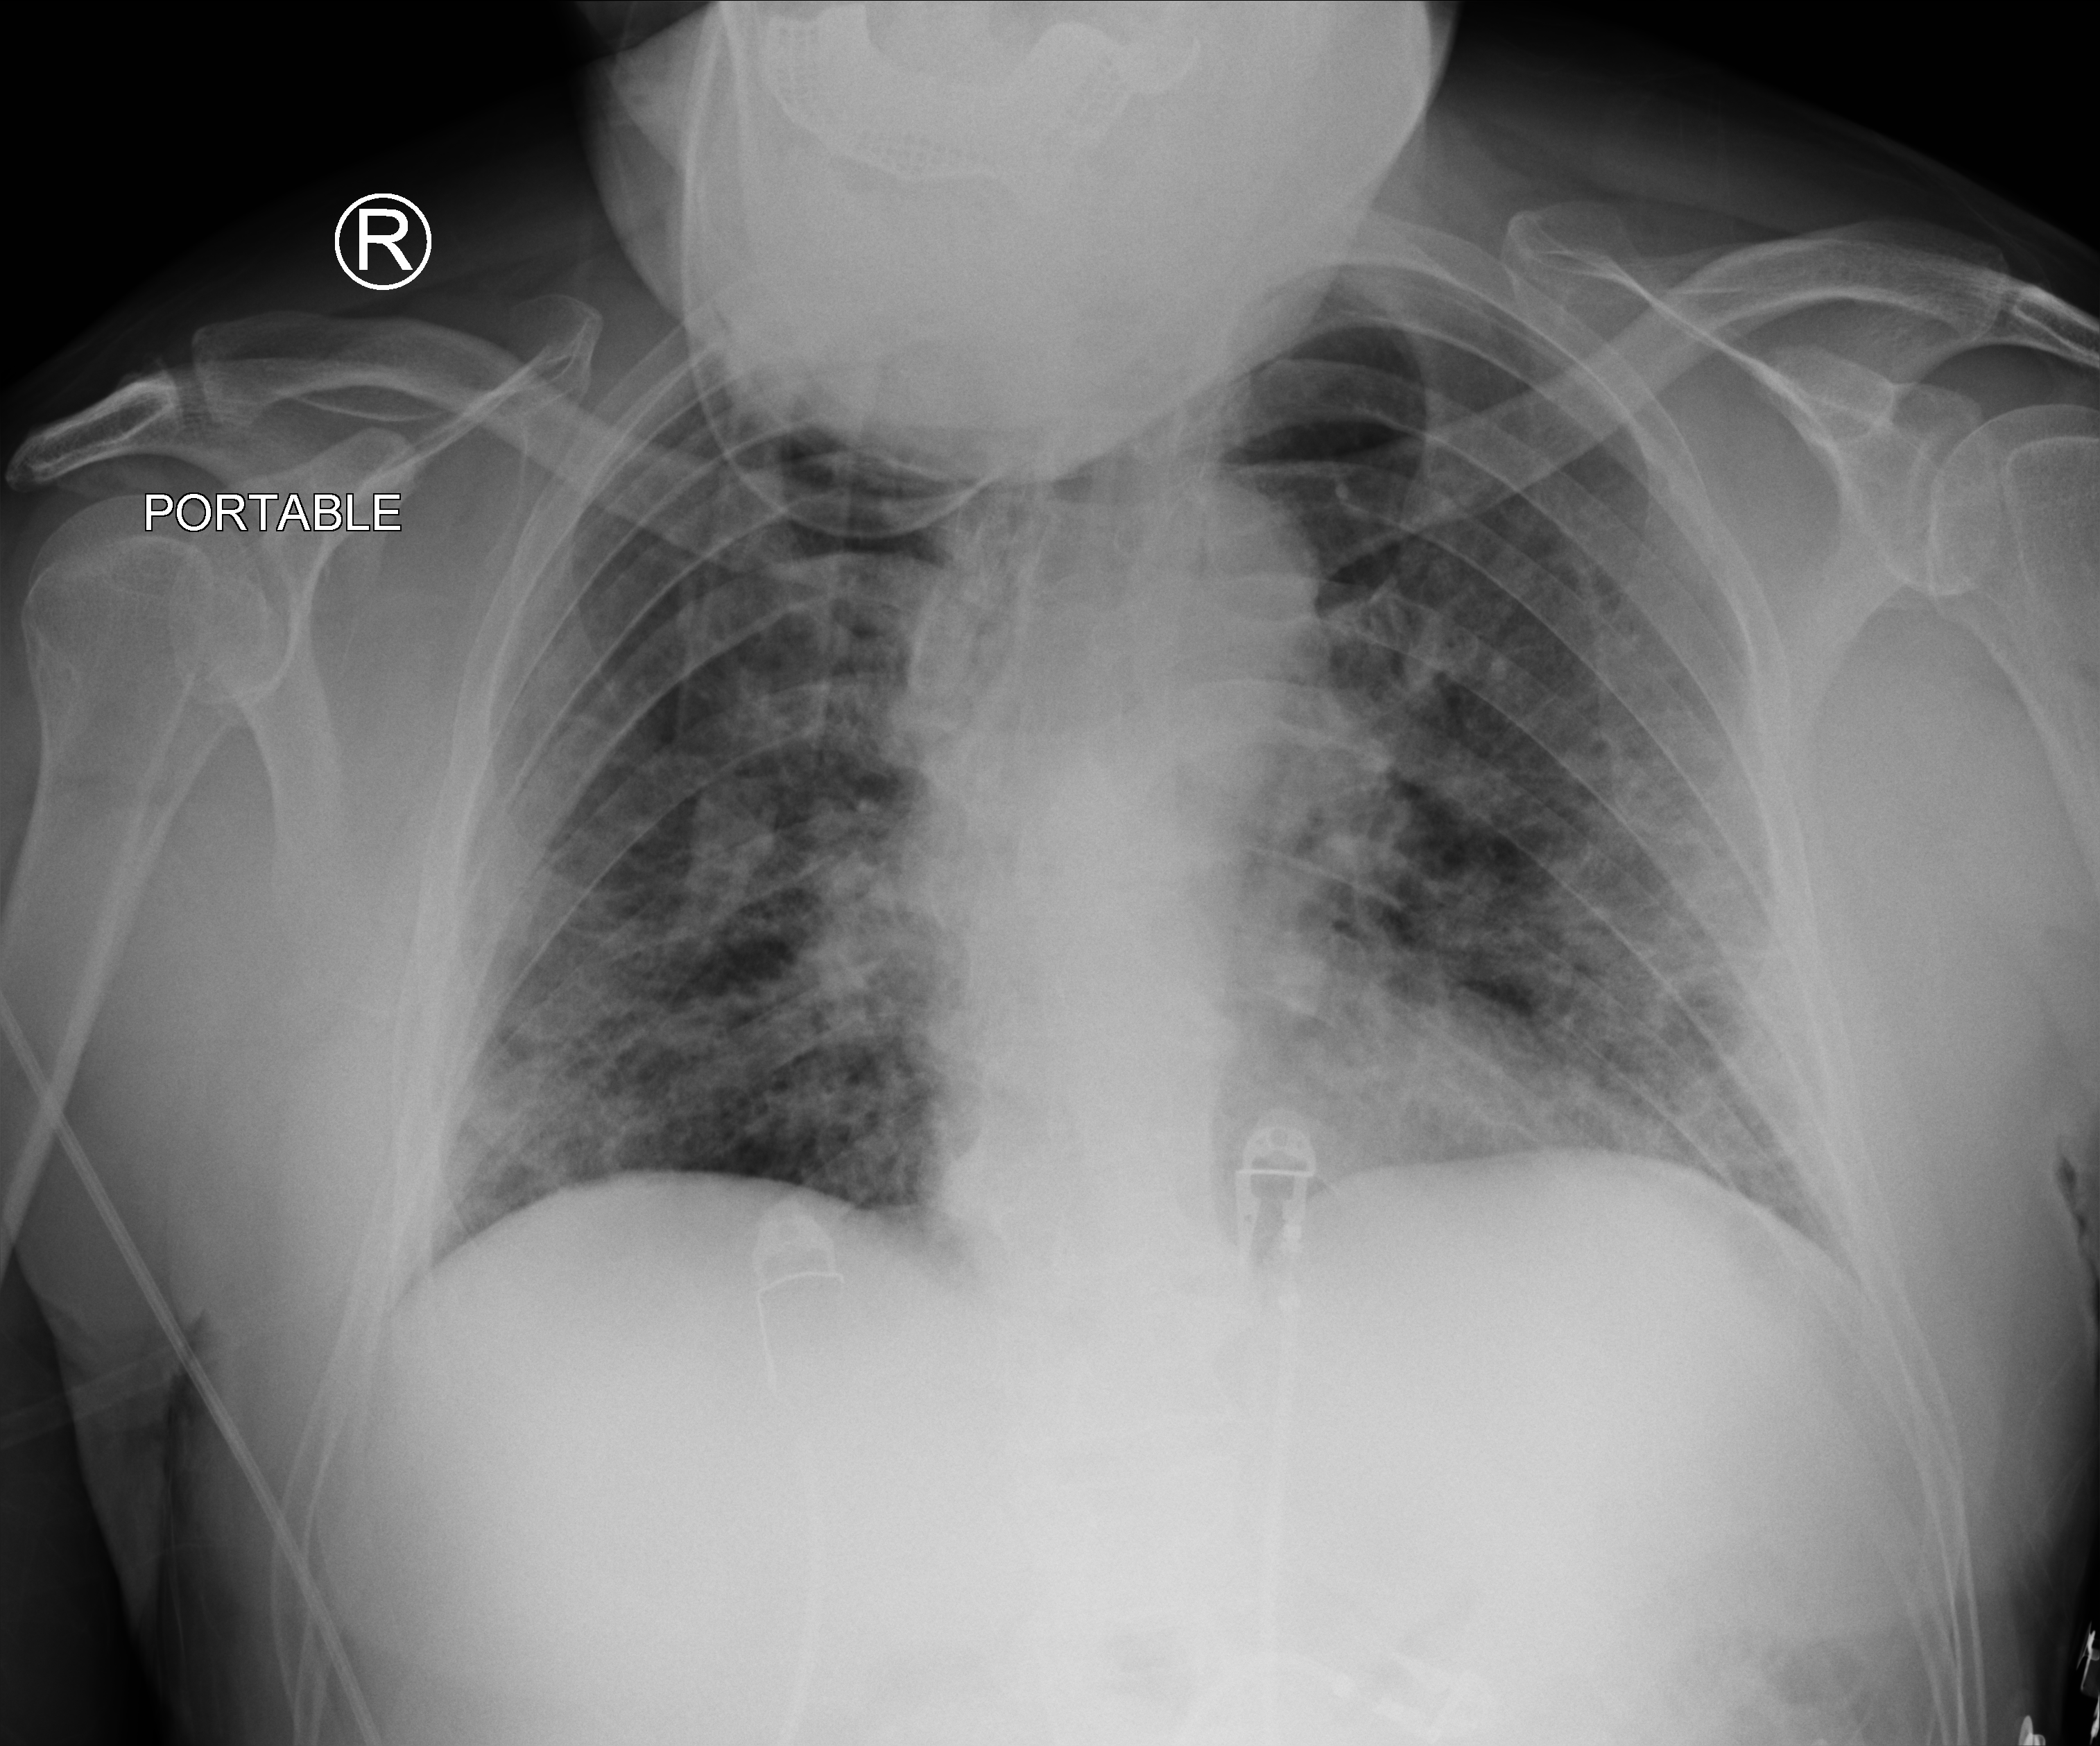
Chest X-ray (portable). Male patient hospitalised with COVID-19, age 60–74 years.
Hospital-stay facts (about this admission, not read from this image; timing relative to this image not recorded): mechanically ventilated during this hospital stay: yes; admitted to intensive care during this hospital stay: yes.